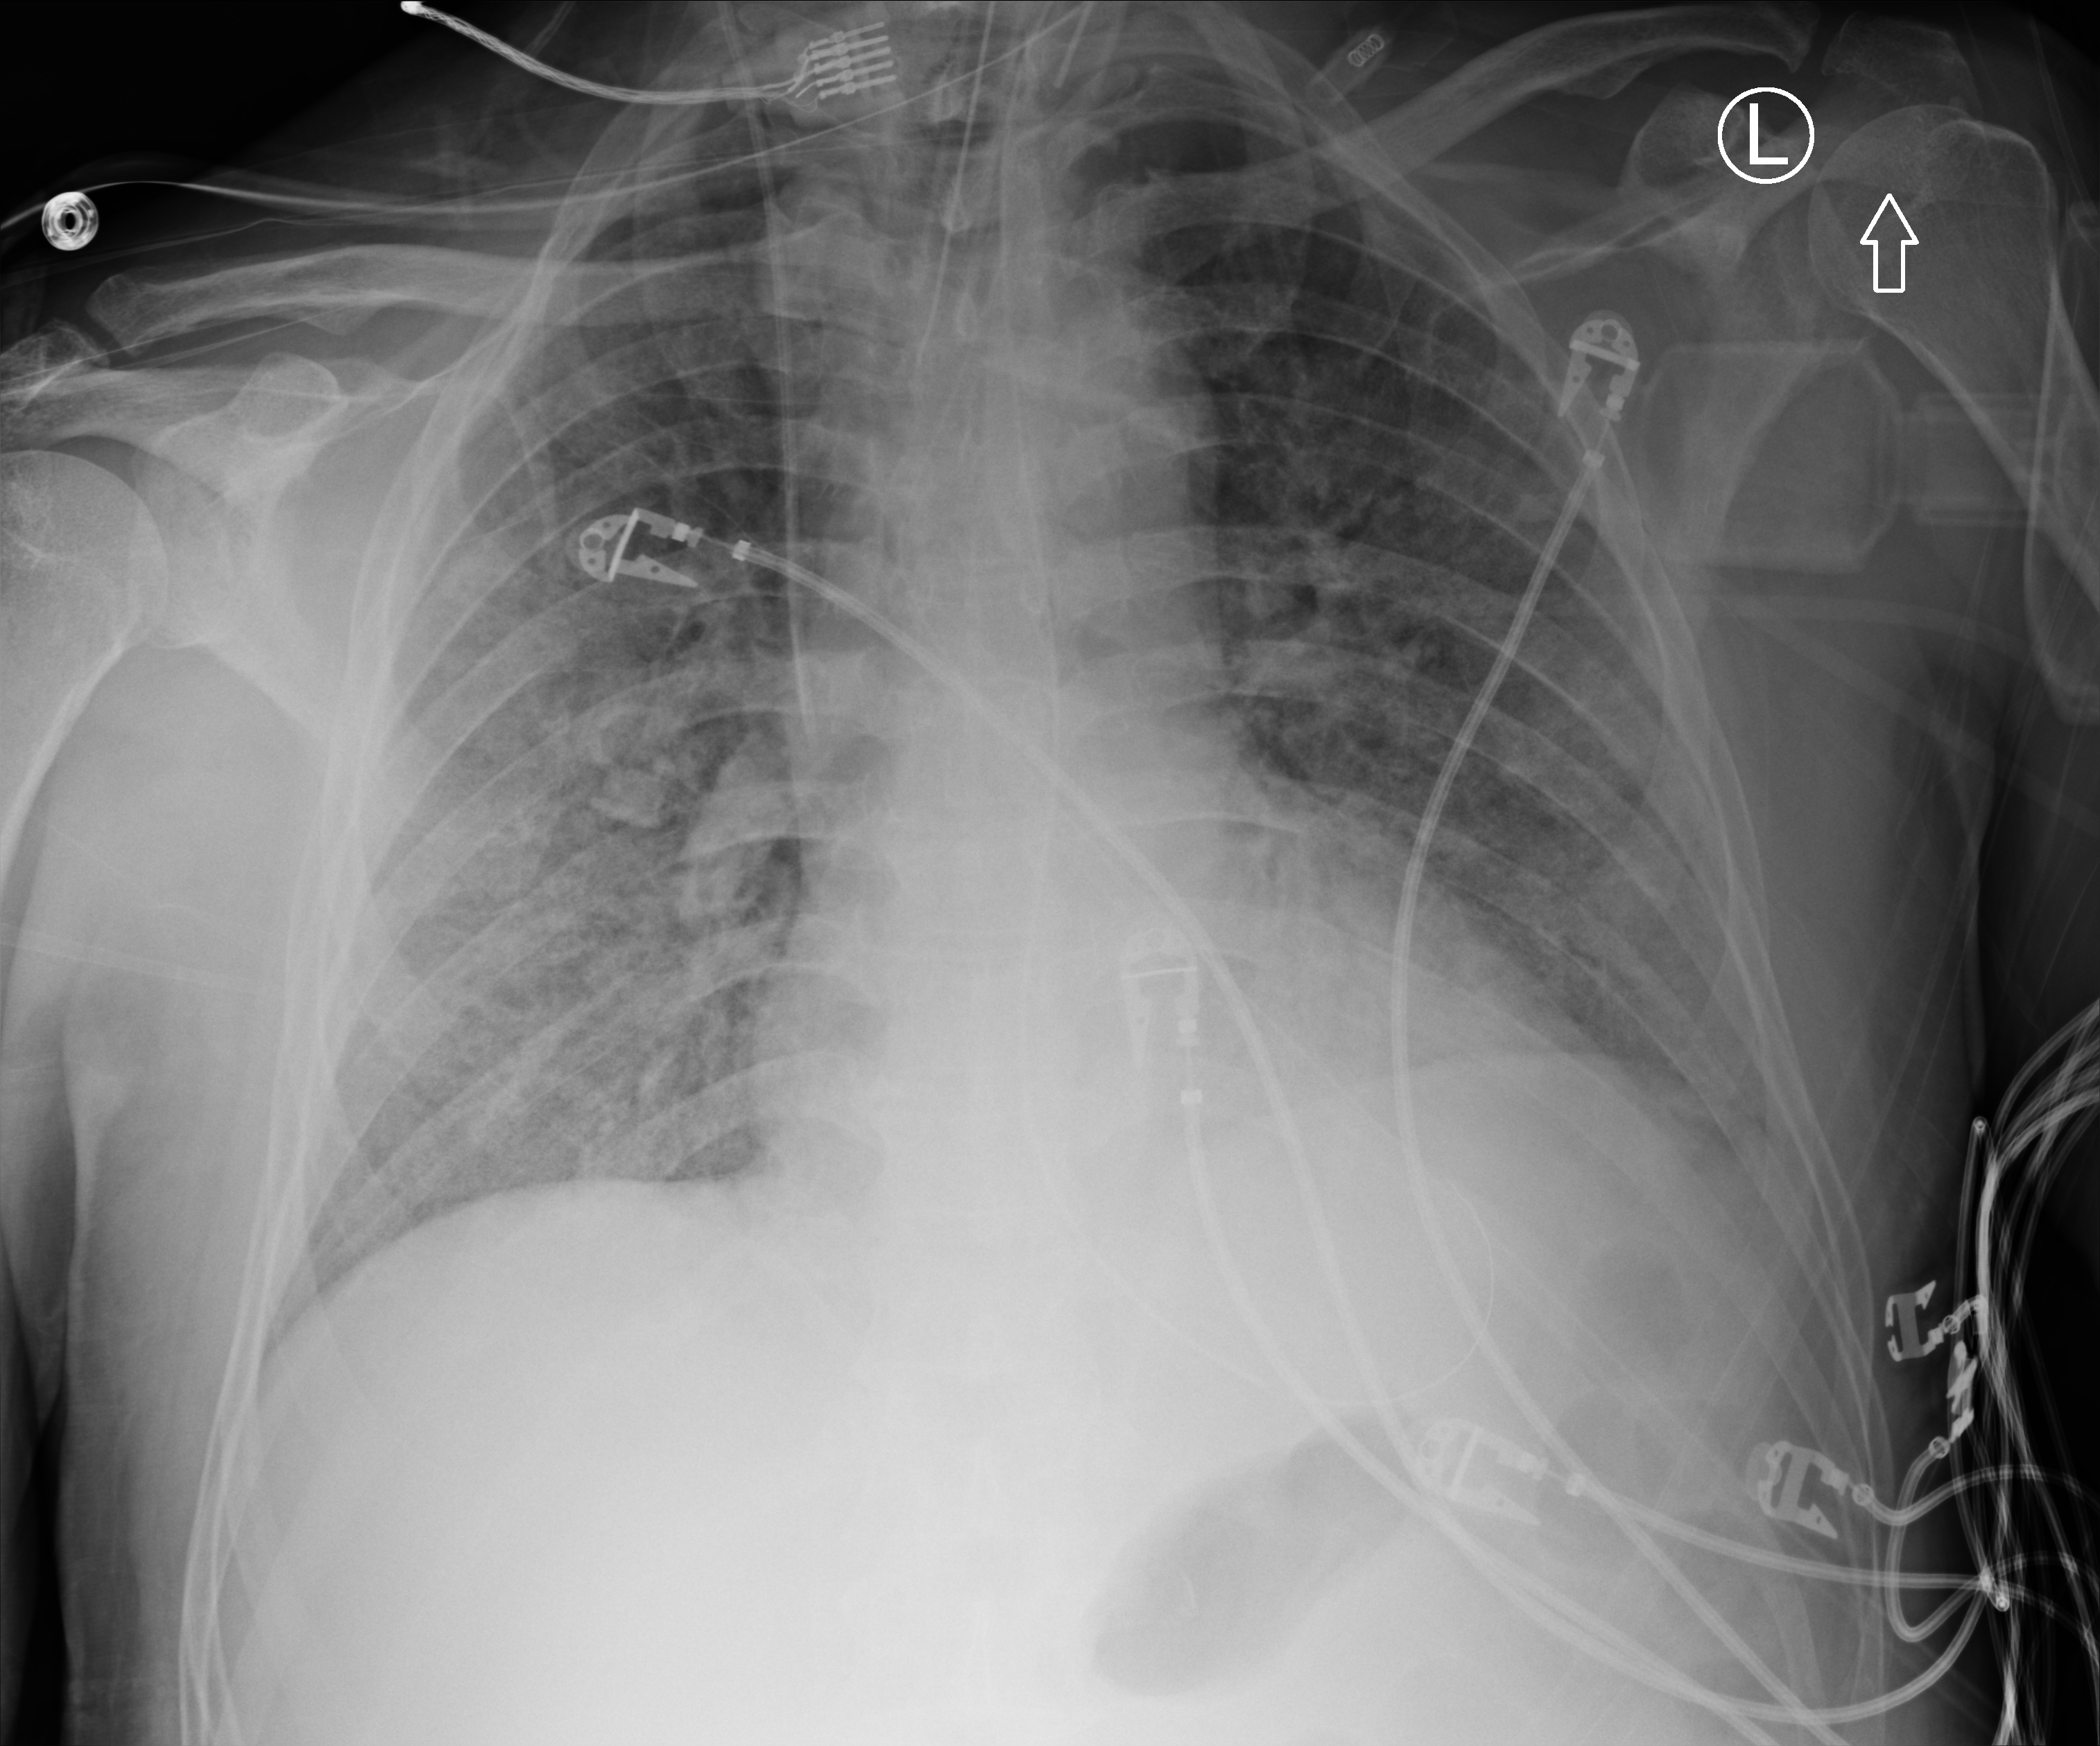
Portable chest radiograph. Patient hospitalised with COVID-19; male, aged 60–74 years.
From the hospital-stay record, not from the radiograph (when in the stay this image was taken is not recorded): hypertension (admission record): yes; admitted to intensive care during this hospital stay: yes.